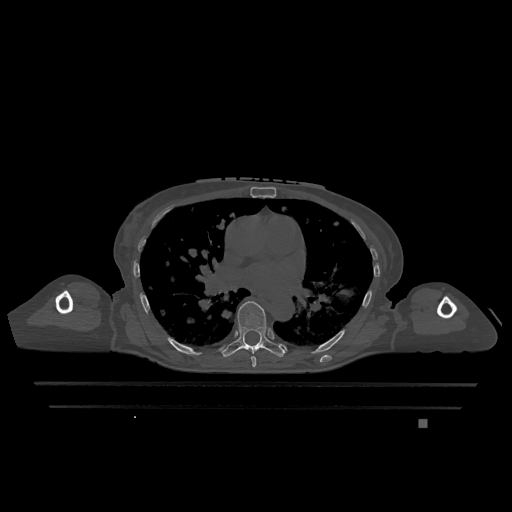
CT including the spine, one axial slice; bone window (W 1800 / L 400 HU); 0.5 mm slice thickness; 512 × 512 image matrix, field of view 500 × 500 mm. Patient: female, 74 years. From the clinical record (not read from this slice): primary cancer: lung; vertebrae with lytic lesions (as recorded): T1, T4, T5, T6, L4, L5.
Outlined on this slice (semi-automatically segmented with operator editing):
- T6 vertebra: box from (x=251, y=356) to (x=256, y=367) px
- T7 vertebra: (x=221, y=301)–(x=287, y=357)